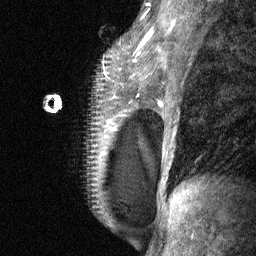
Breast MRI (dynamic contrast-enhanced), one sagittal slice; dynamic contrast-enhanced study with each time point stored as its own series, time point 2 of 3 at this slice position (early post-contrast, ordered by acquisition time); 1.5 T; TE 4.8 ms, TR 27 ms; 2 mm slice thickness; 256 × 256 image matrix. Patient: female, 34 years. From the clinical record (not read from this slice): setting: breast cancer imaged before/during neoadjuvant chemotherapy; receptor status: HR-positive, HER2-negative.
Structures marked on this image (semi-automatic segmentation, software-assisted and operator-edited):
- analysis volume of interest (the breast-tissue region the enhancement analysis was run in; not a lesion): box from (x=43, y=23) to (x=157, y=197) px
- tumour enhancement mask (voxels above the 90 % enhancement threshold inside the analysis volume of interest): (x=110, y=32)–(x=151, y=129)